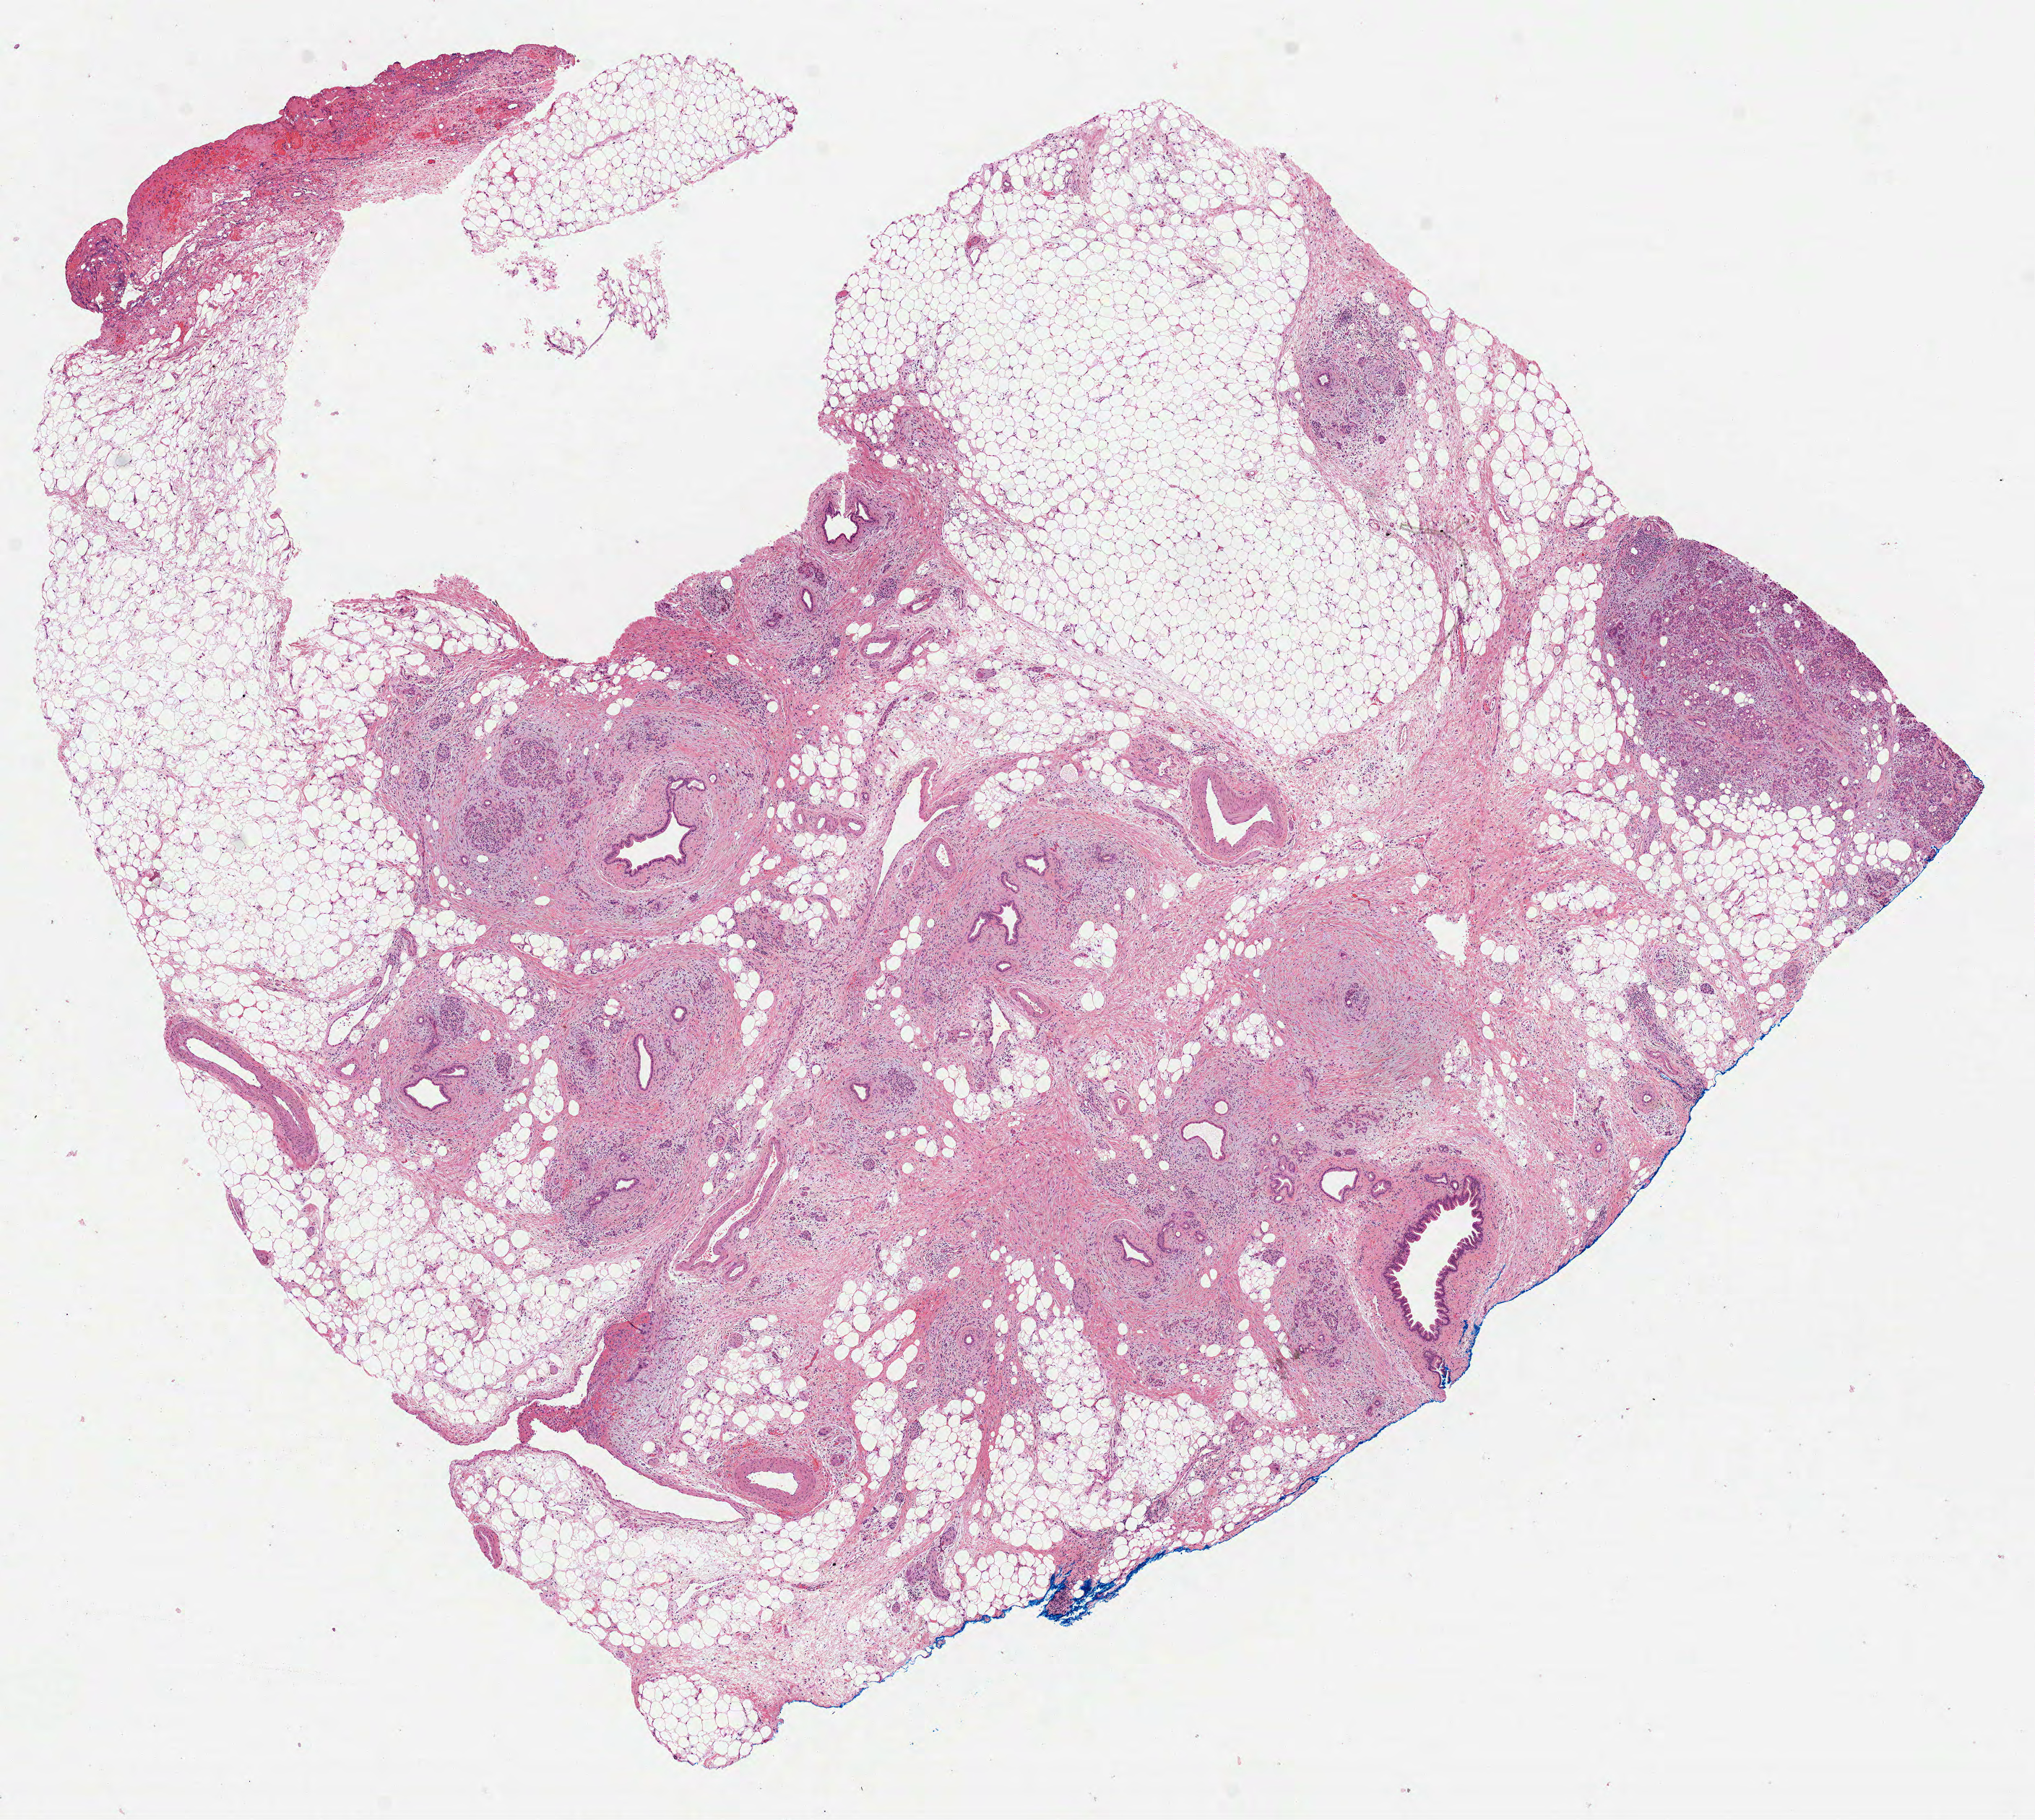
Hematoxylin and eosin (H&E) stained whole-slide image — whole scanned area (about 11.4 x 10.2 mm, slide scanned at 40x) shown as a low-resolution overview. Formalin-fixed paraffin-embedded (FFPE) diagnostic section. Primary tumour sample from the pancreas. Male, age 61 years at initial diagnosis. Histologic grade: G2 (moderately differentiated).
• lymph nodes positive (case pathology): 4 of 33 examined
• pathologic diagnosis: Infiltrating duct carcinoma, NOS (head of pancreas)
• AJCC pathologic stage: IIB